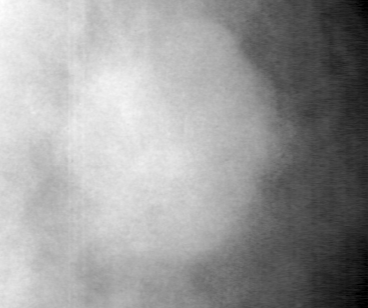
Cropped region of a digitized screen-film mammogram centred on a radiologist-marked abnormality; right breast; CC view.
Marked abnormality: mass, shape lobulated, margins microlobulated; BI-RADS assessment category 4; subtlety rating 4 on a 1 (subtle) to 5 (obvious) scale; pathology (as recorded): benign.